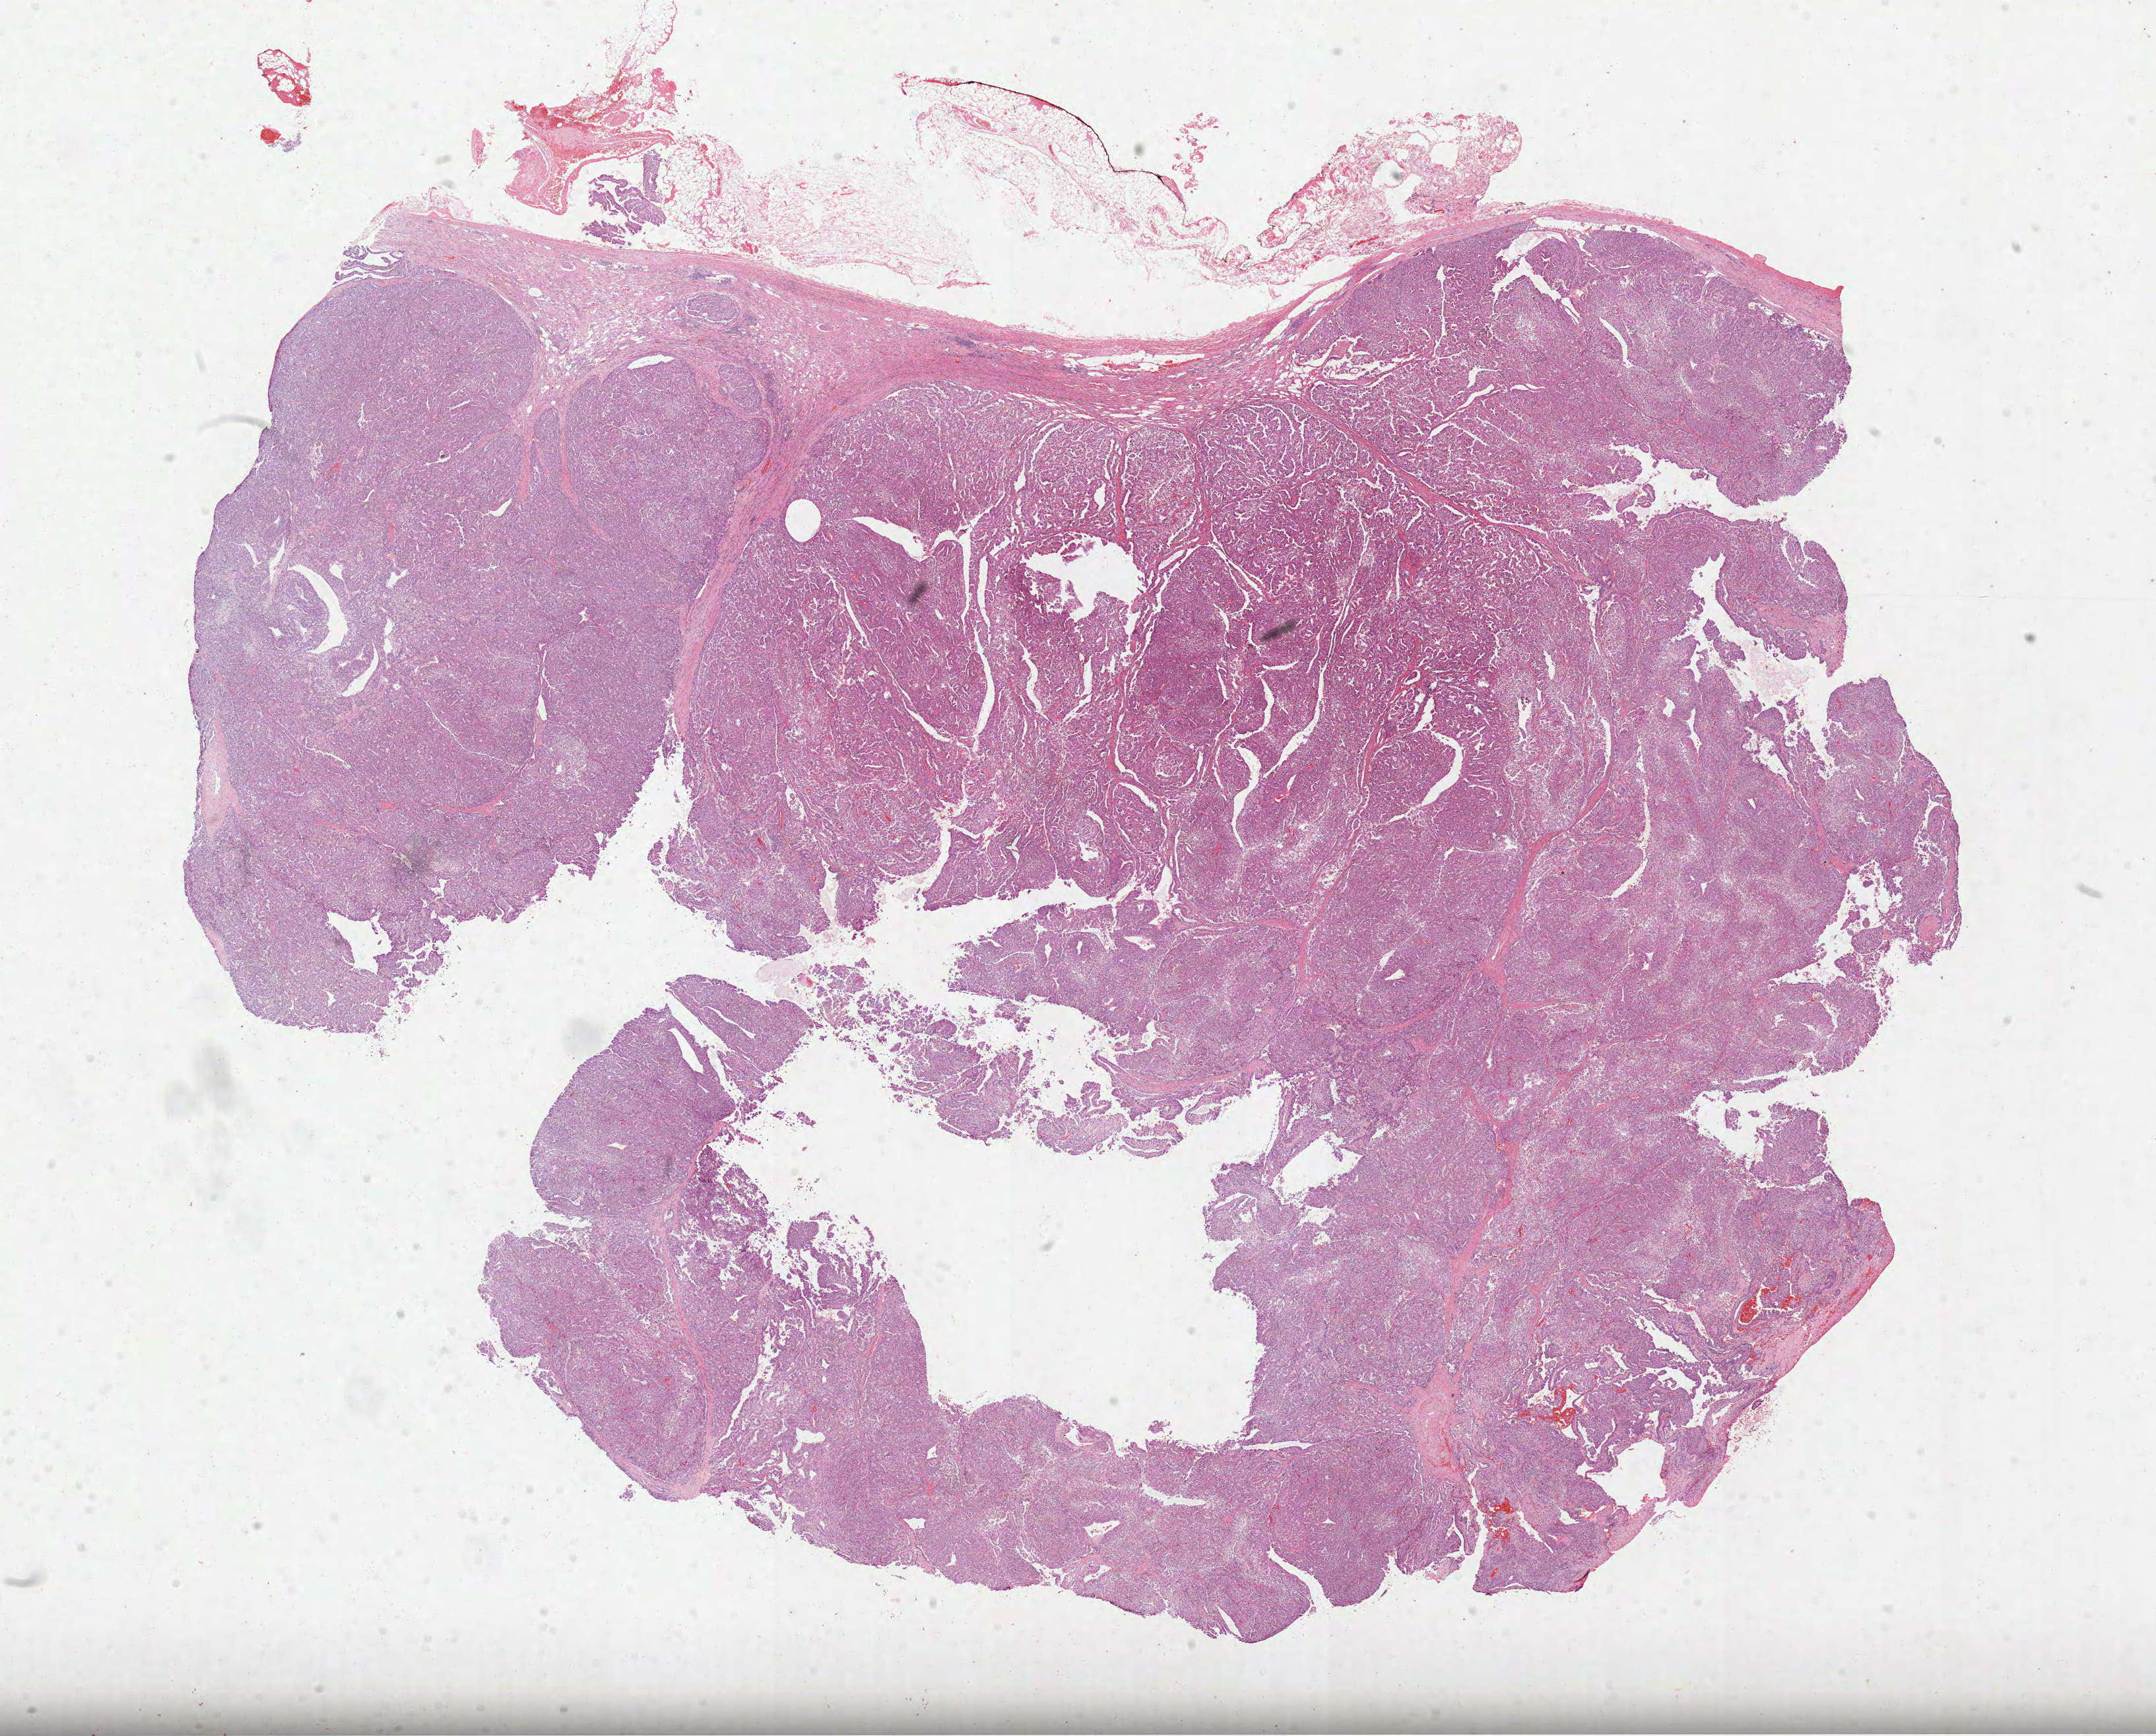
Hematoxylin and eosin (H&E) stained whole-slide image — shown as a low-resolution overview of the whole scanned area (about 26.3 x 21.2 mm, acquisition: 40x scan), formalin-fixed paraffin-embedded (FFPE) diagnostic section, primary tumour sample from the kidney. Female, age 55 years at initial diagnosis.
Laterality: left. Pathologic diagnosis: Papillary adenocarcinoma, NOS. AJCC pathologic stage: III.